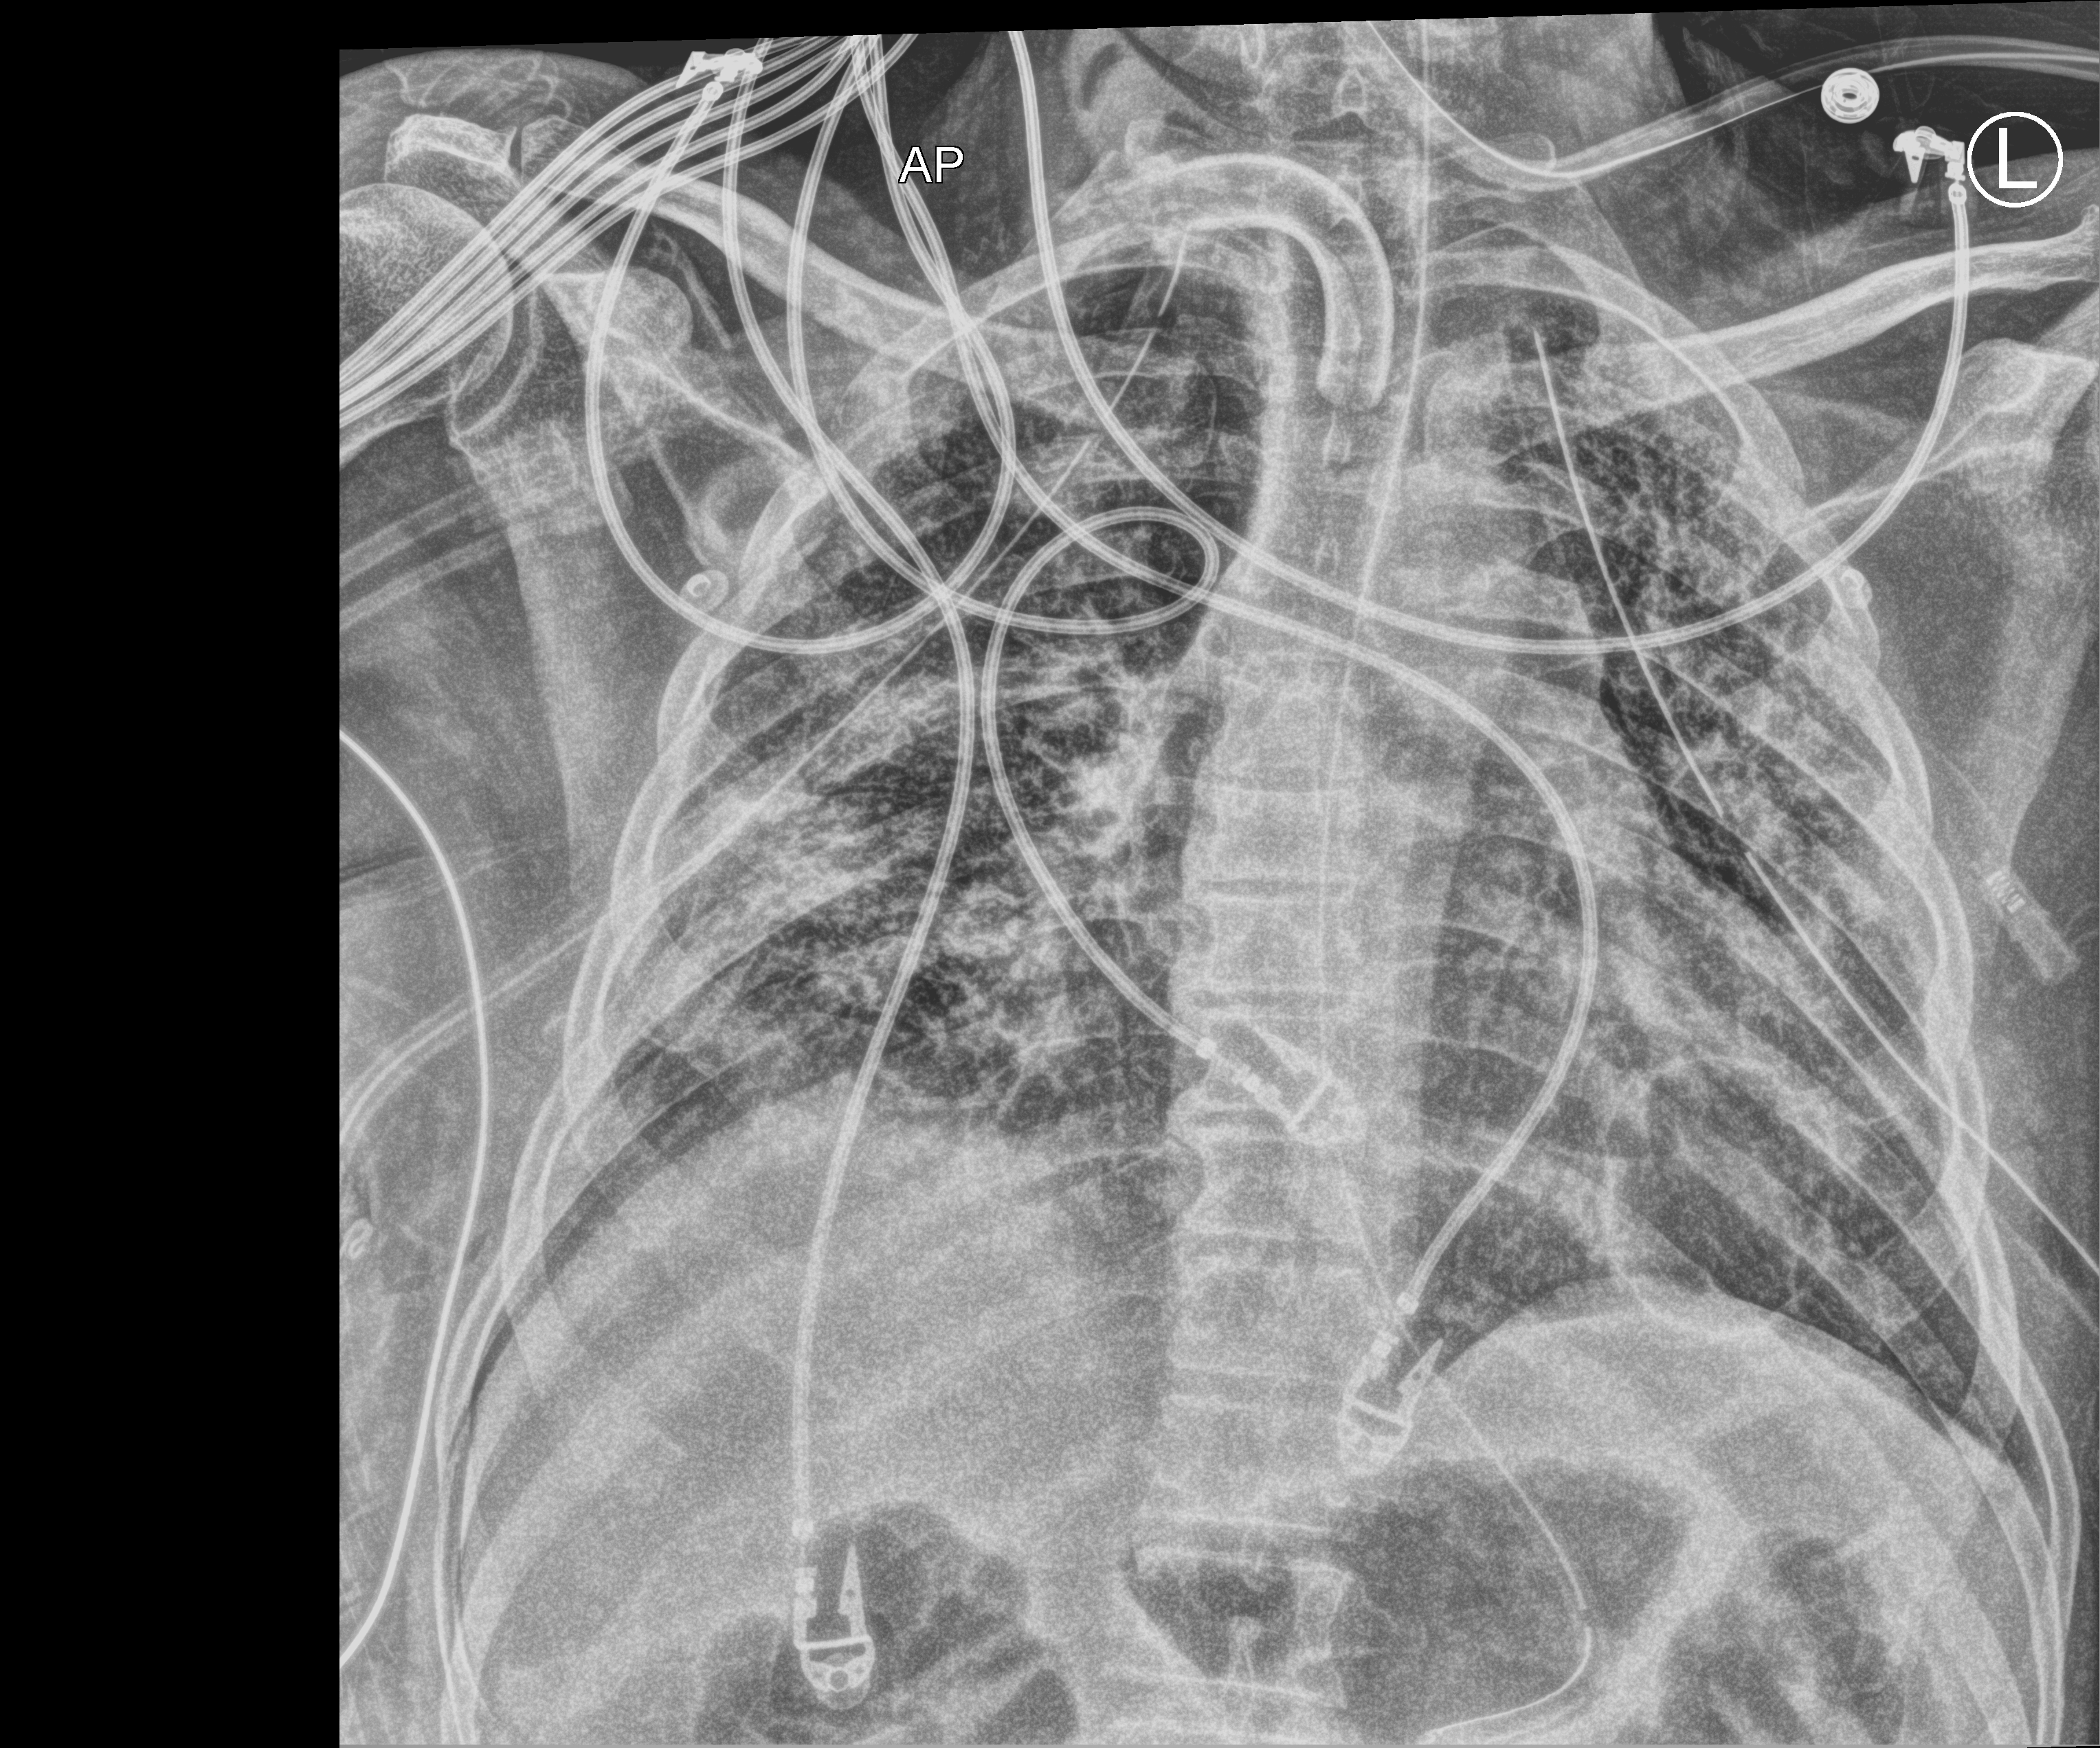
Bedside chest radiograph (computed radiography), anteroposterior (AP) projection. Patient hospitalised with COVID-19; male, aged 18–59 years.
From the hospital-stay record, not from the radiograph (when in the stay this image was taken is not recorded): COPD (admission record): no.